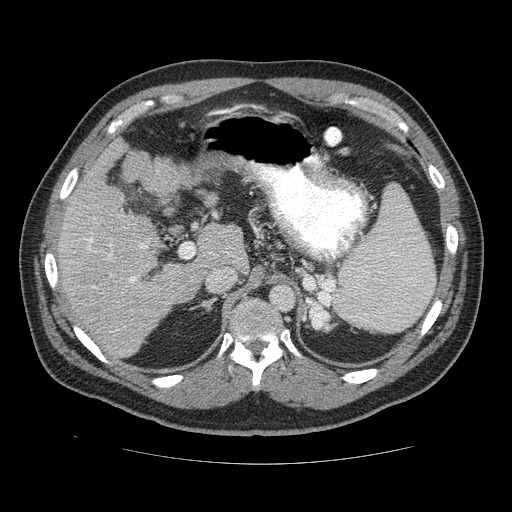
Contrast-enhanced abdominal CT (liver protocol), one axial slice. Position 83 of 113 along the scan axis. Reconstruction kernel STANDARD. Soft-tissue window (W 400 / L 40 HU). 512 × 512 image matrix, field of view 400 × 400 mm. From the clinical record (not read from this slice): diagnosis: hepatocellular carcinoma (patient treated with transarterial chemoembolisation; whether this scan precedes or follows treatment is not stated here); TNM stage (as recorded): Stage-II; Child-Pugh class: B; tumour differentiation: moderately differentiated; tumour nodularity: multinodular.
Outlined on this slice (semi-automatic segmentation, software-assisted and operator-edited):
- liver parenchyma outside the tumour (the mass and vessels are separate outlines, so this box may not span the whole liver): box from (x=50, y=136) to (x=246, y=358) px
- liver vessels: (x=79, y=218)–(x=213, y=284)